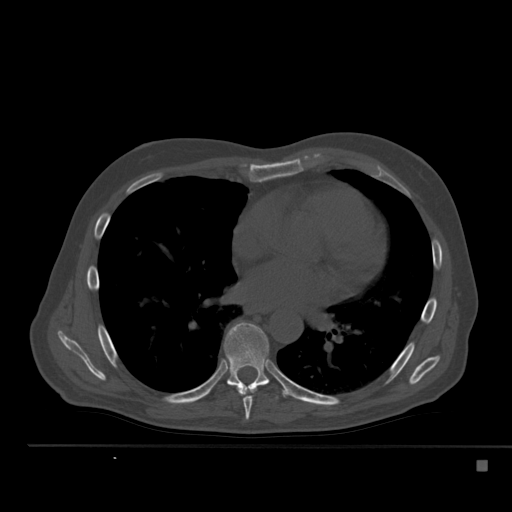
CT including the spine, one axial slice. Position 316 of 517 along the scan axis. Reconstruction kernel Br40s. Bone window (W 1800 / L 400 HU). 1.5 mm slice thickness. 512 × 512 image matrix. Male patient, age 70 years. Case-level facts recorded for this patient, not image findings: primary cancer: renal.
Annotated regions visible in this slice (semi-automatically segmented with operator editing):
- T7 vertebra: bounding box <235,385,253,420> (left, top, right, bottom; pixels)
- T8 vertebra: <224,323,288,400>